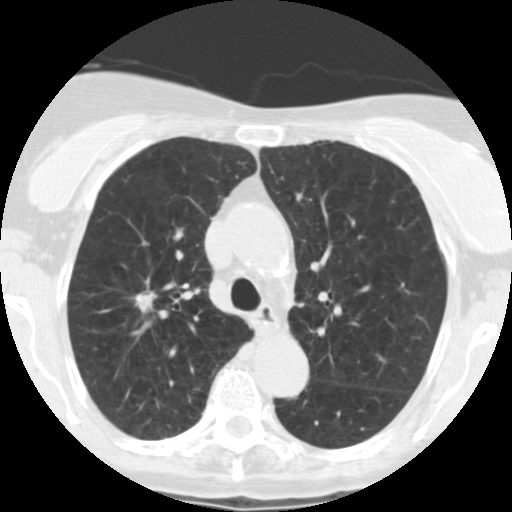
Axial slice from a low-dose chest CT screening exam; baseline annual screen; lung window (W 1500 / L -600 HU); 512 × 512 image matrix. Female, age 67 years at enrolment.
• Expert reader's lesion annotation, bounding box (x1, y1, x2, y2) in pixels: (114, 281, 171, 323).
• The screening reader recorded 6 non-calcified nodules or masses ≥4 mm on this exam (right upper lobe, right middle lobe, left lower lobe, right middle lobe, left lower lobe, left lower lobe); which of them this box marks is not recorded.
• Official screen result: positive, change unspecified: nodule(s) >= 4 mm or enlarging nodule(s), mass(es), or other non-specific abnormalities suspicious for lung cancer.
• Participant outcome: lung cancer diagnosed 15 days after this screen — adenocarcinoma, NOS, right upper lobe, moderately differentiated (G2), stage IA (AJCC 6th edition), 14 mm at pathology.